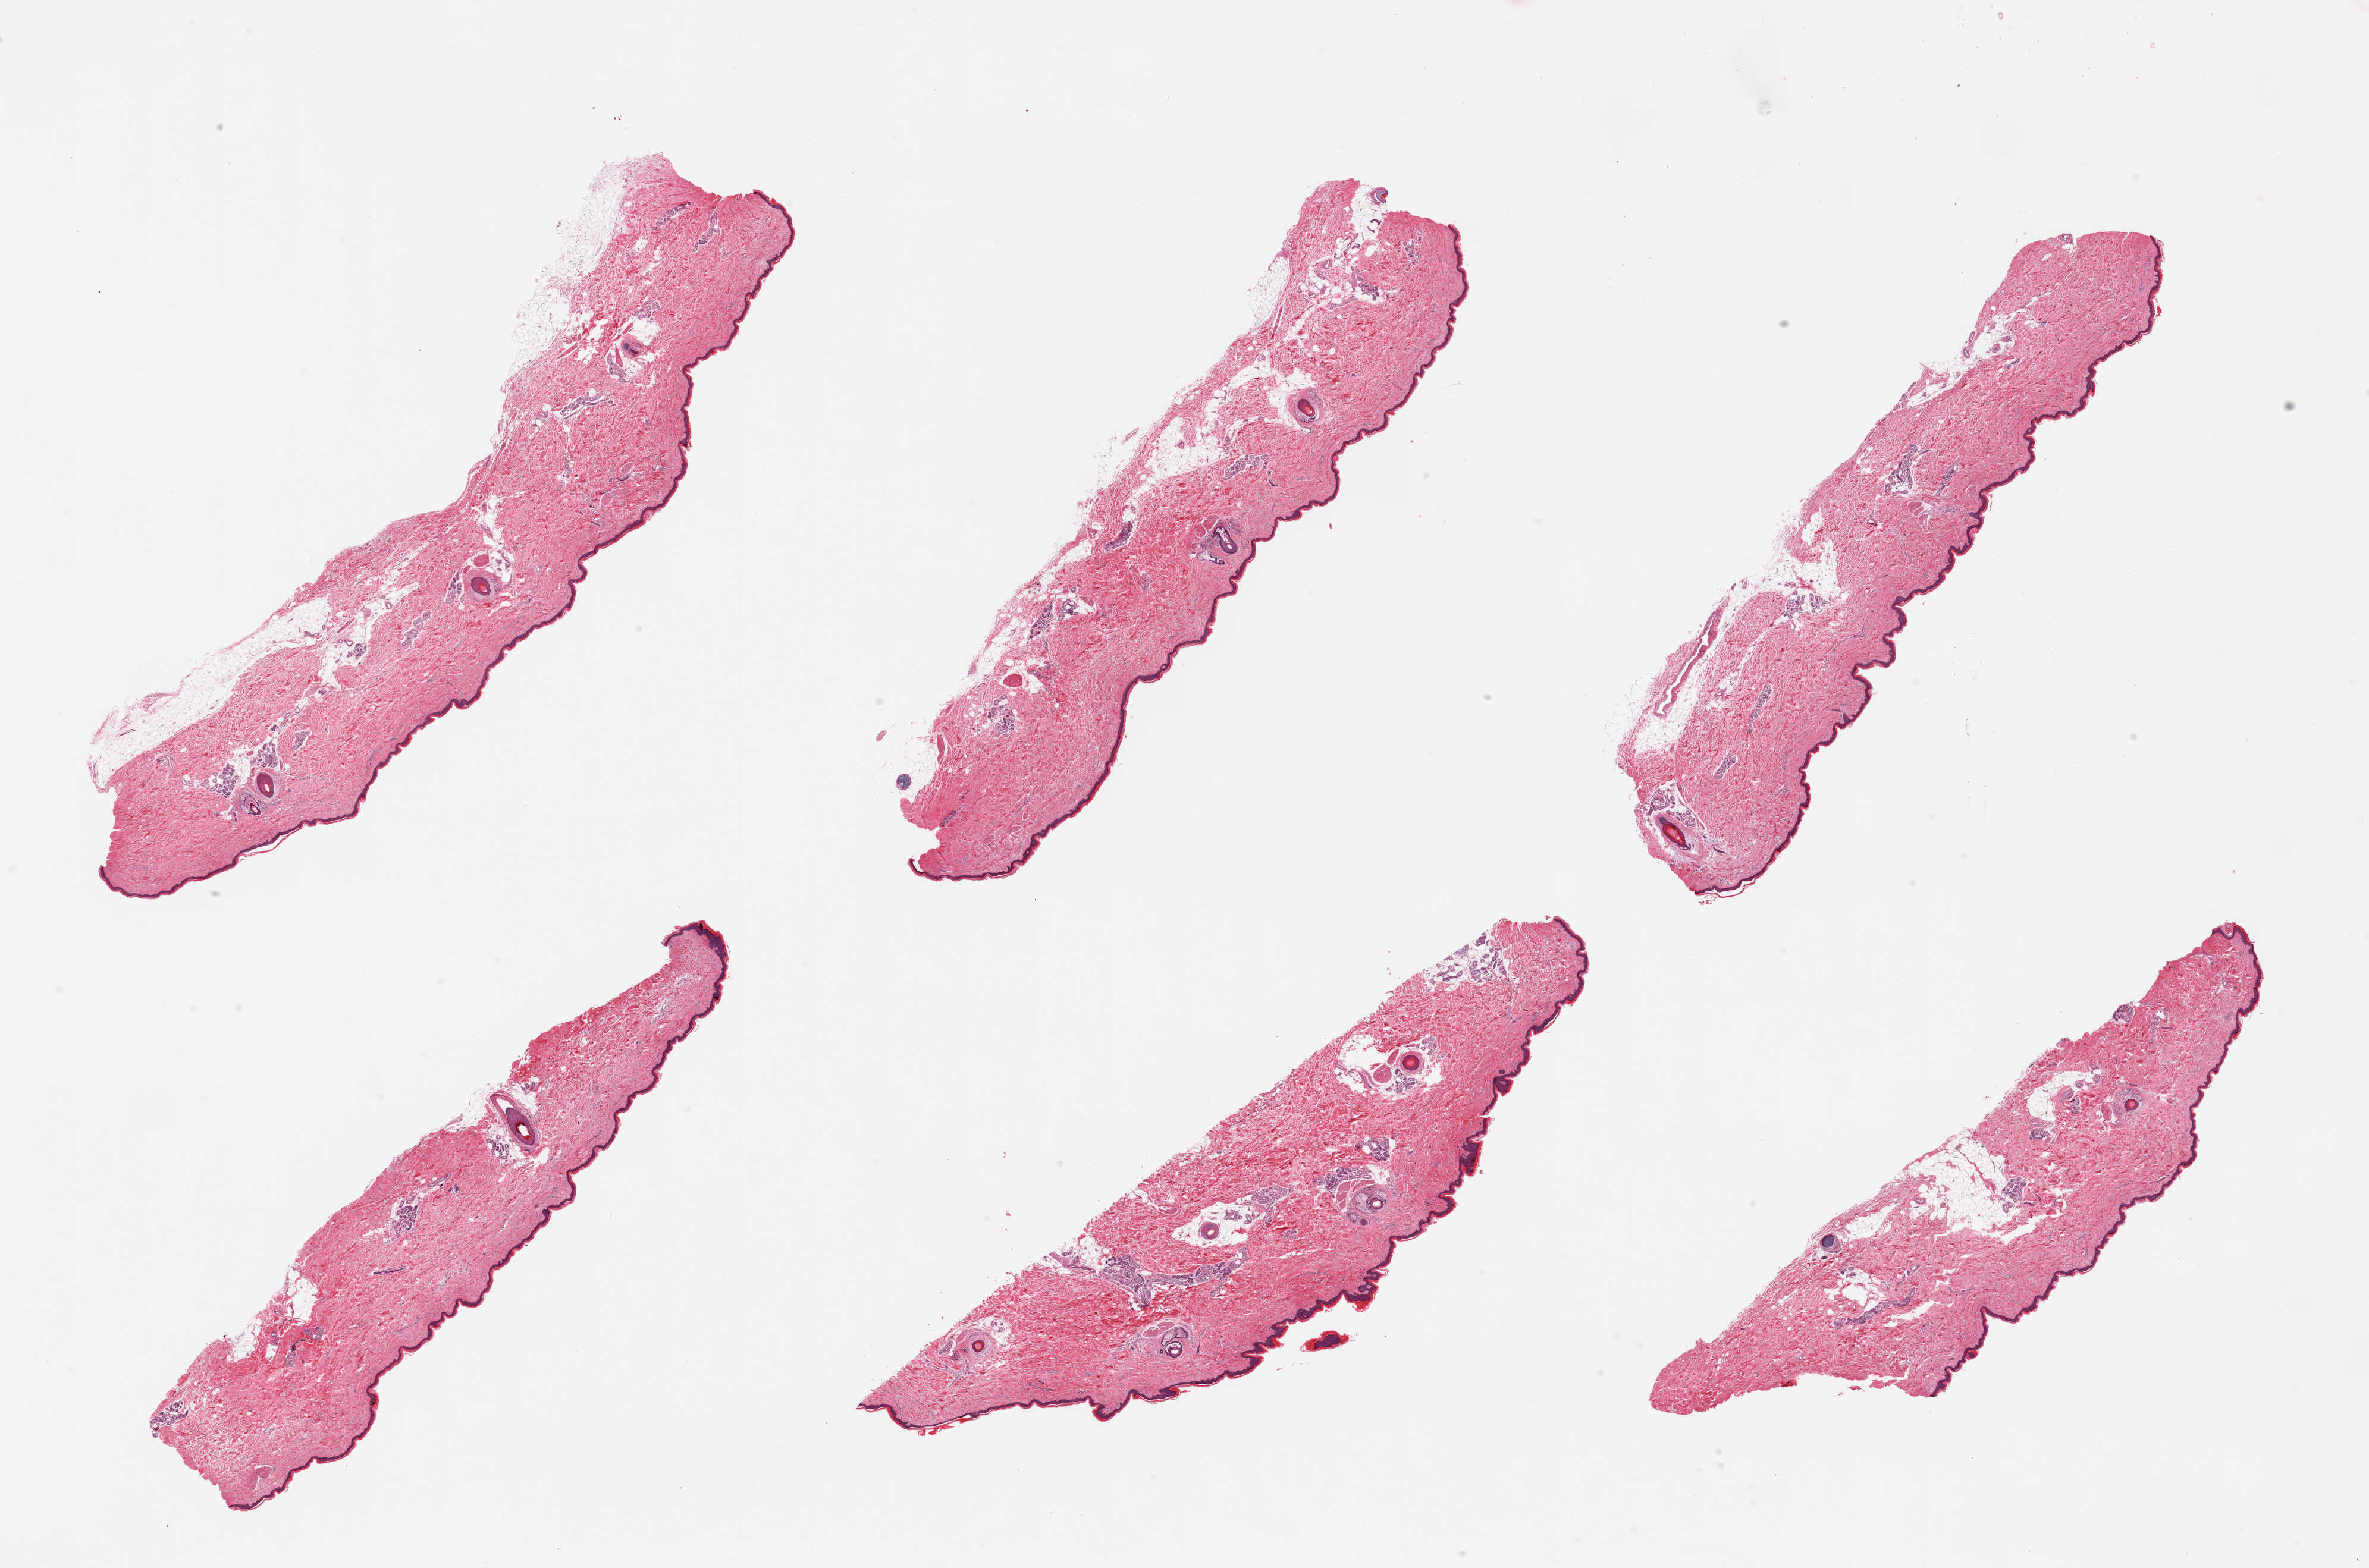
Whole-slide image, hematoxylin and eosin (H&E) stain, brightfield — shown as a low-resolution overview of the whole scanned area (about 31.5 x 20.9 mm); PAXgene-fixed, paraffin-embedded tissue; target tissue: skin of lower leg; tissue donor sample. Male donor.
- review note (as recorded): 6 pieces, squamous epithelium is ~40 microns, few foci of adherent dermal fat